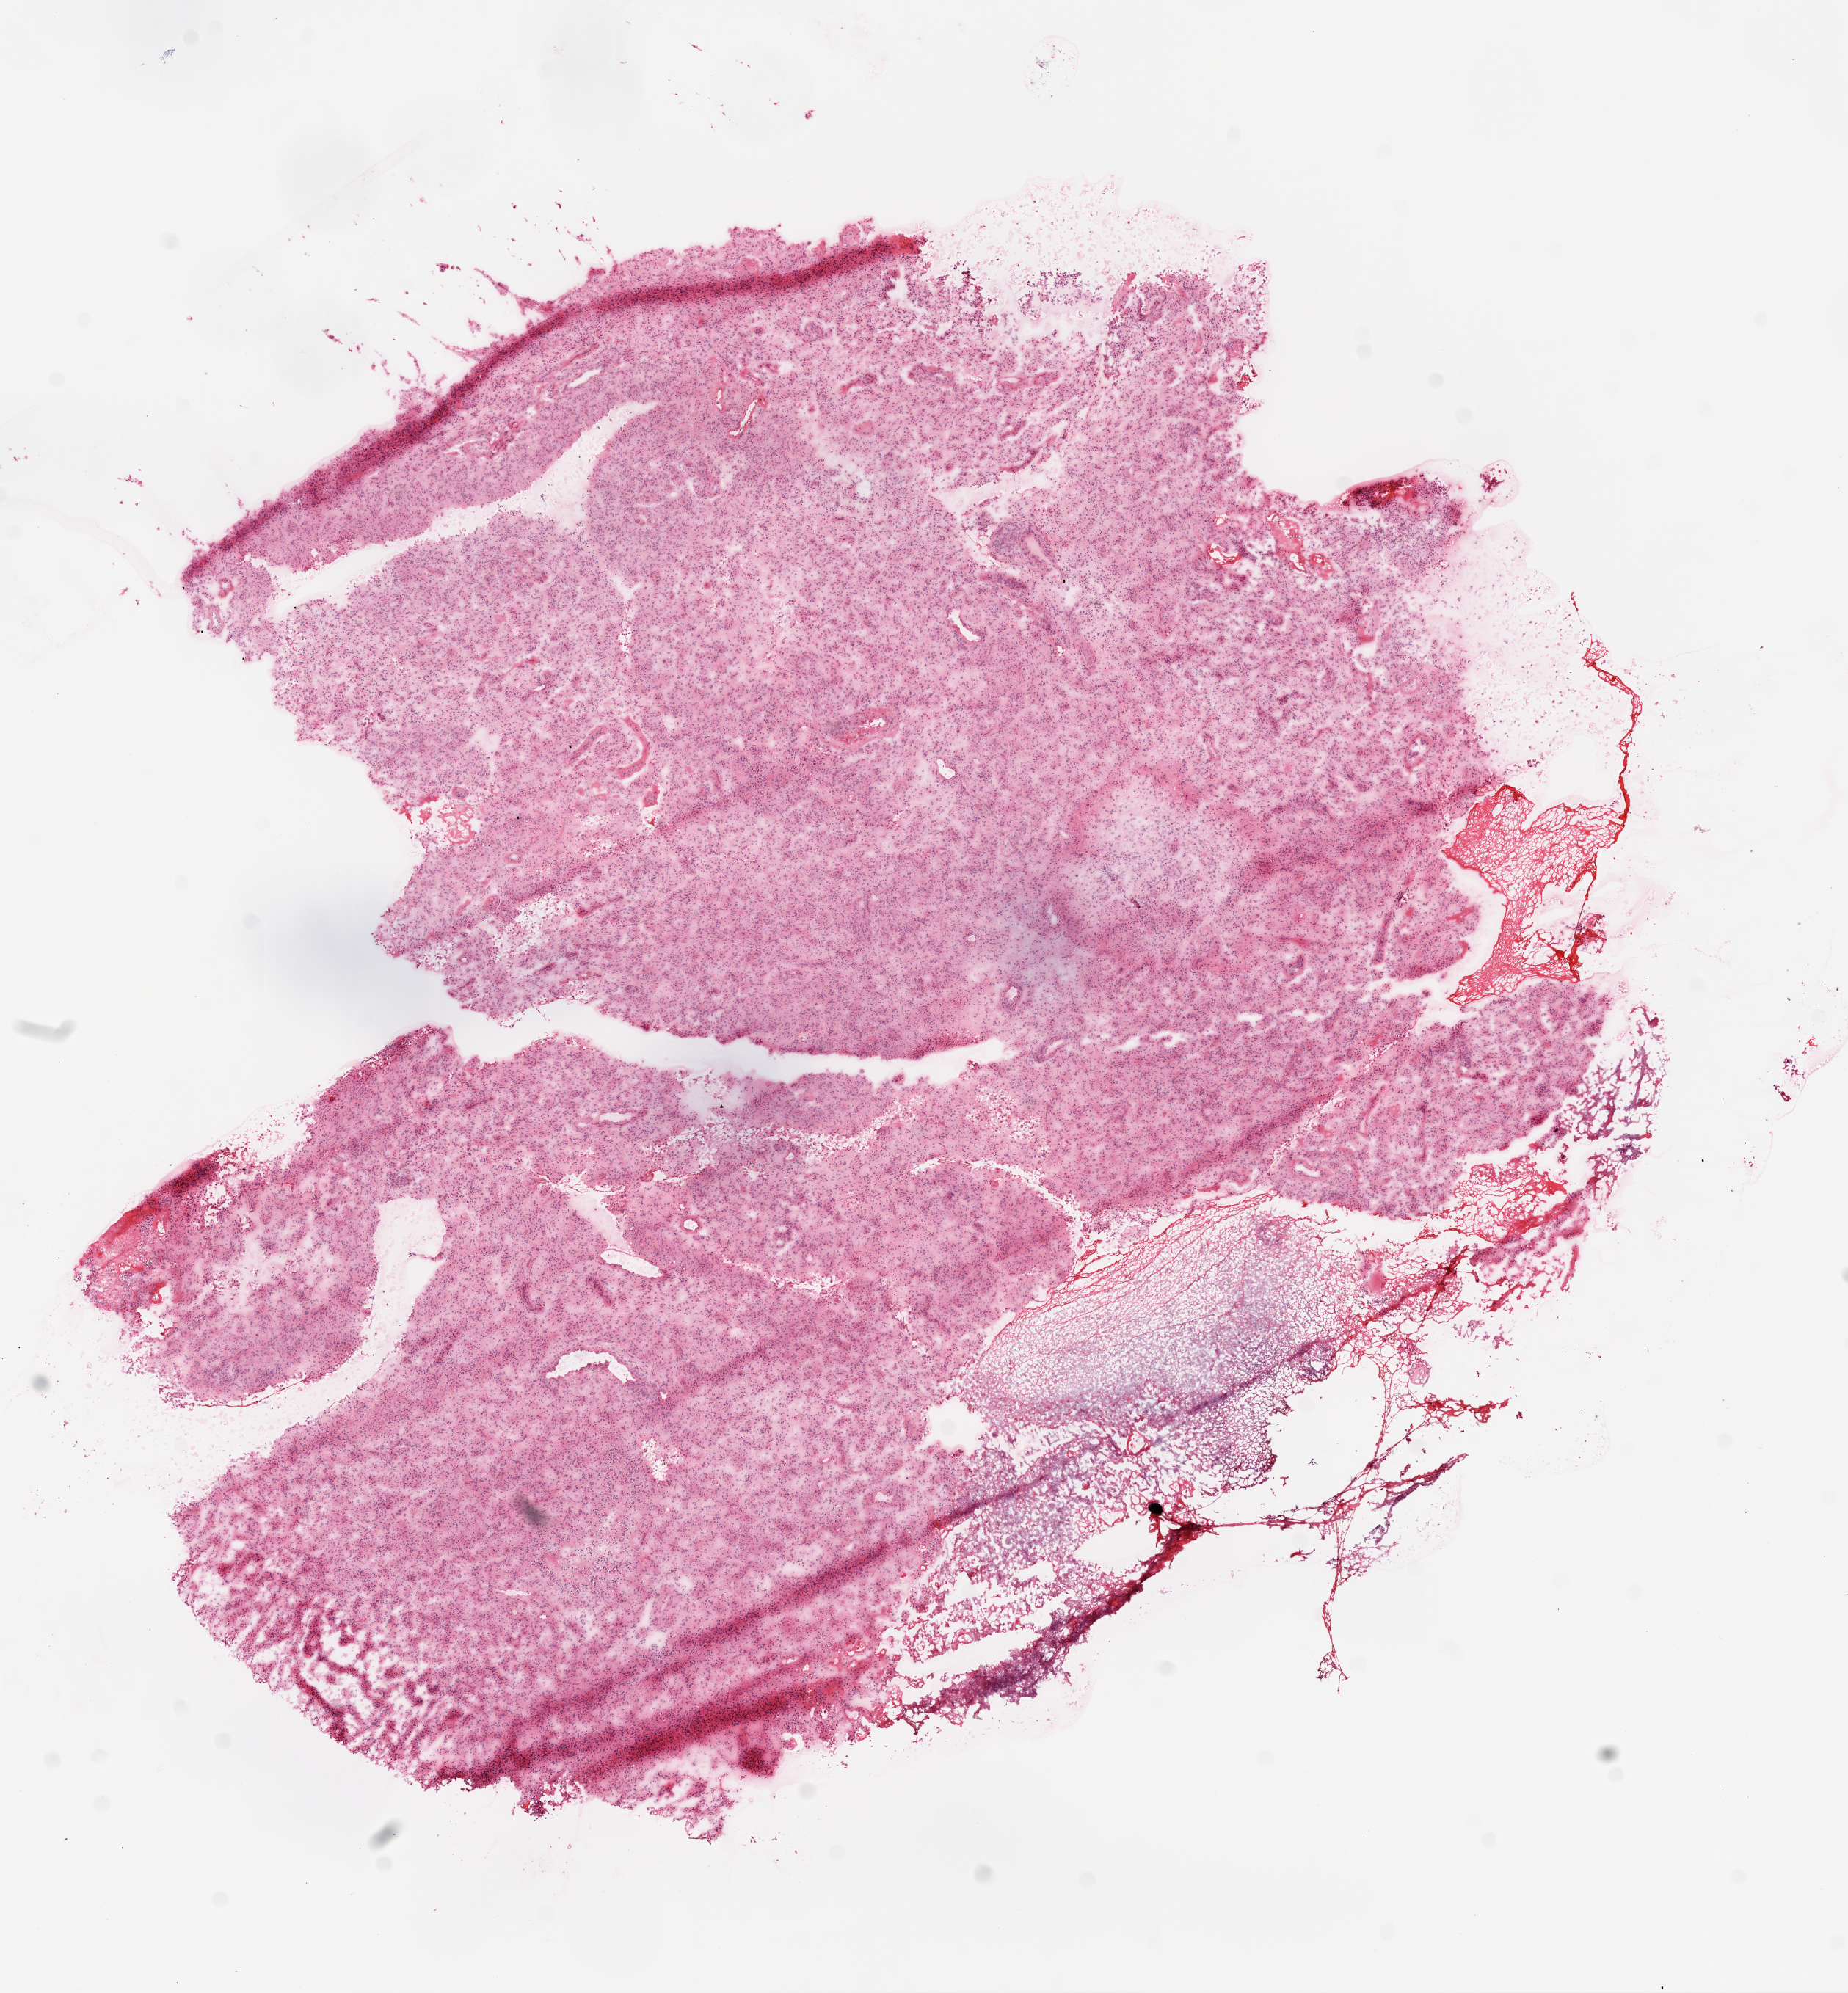
Hematoxylin and eosin (H&E) stained whole-slide image, a low-resolution overview of the entire scanned area, about 10.2 x 11.0 mm (slide scanned at 20x); frozen section from the bottom of the tissue portion; brain, primary tumour sample. Male, age 69 years at initial diagnosis. Pathologist review of this section (percent, as recorded): tumour cells 90%, tumour nuclei 95%, normal cells 0%, stromal cells 0%, necrosis 10%.
Diagnosis: Glioblastoma.